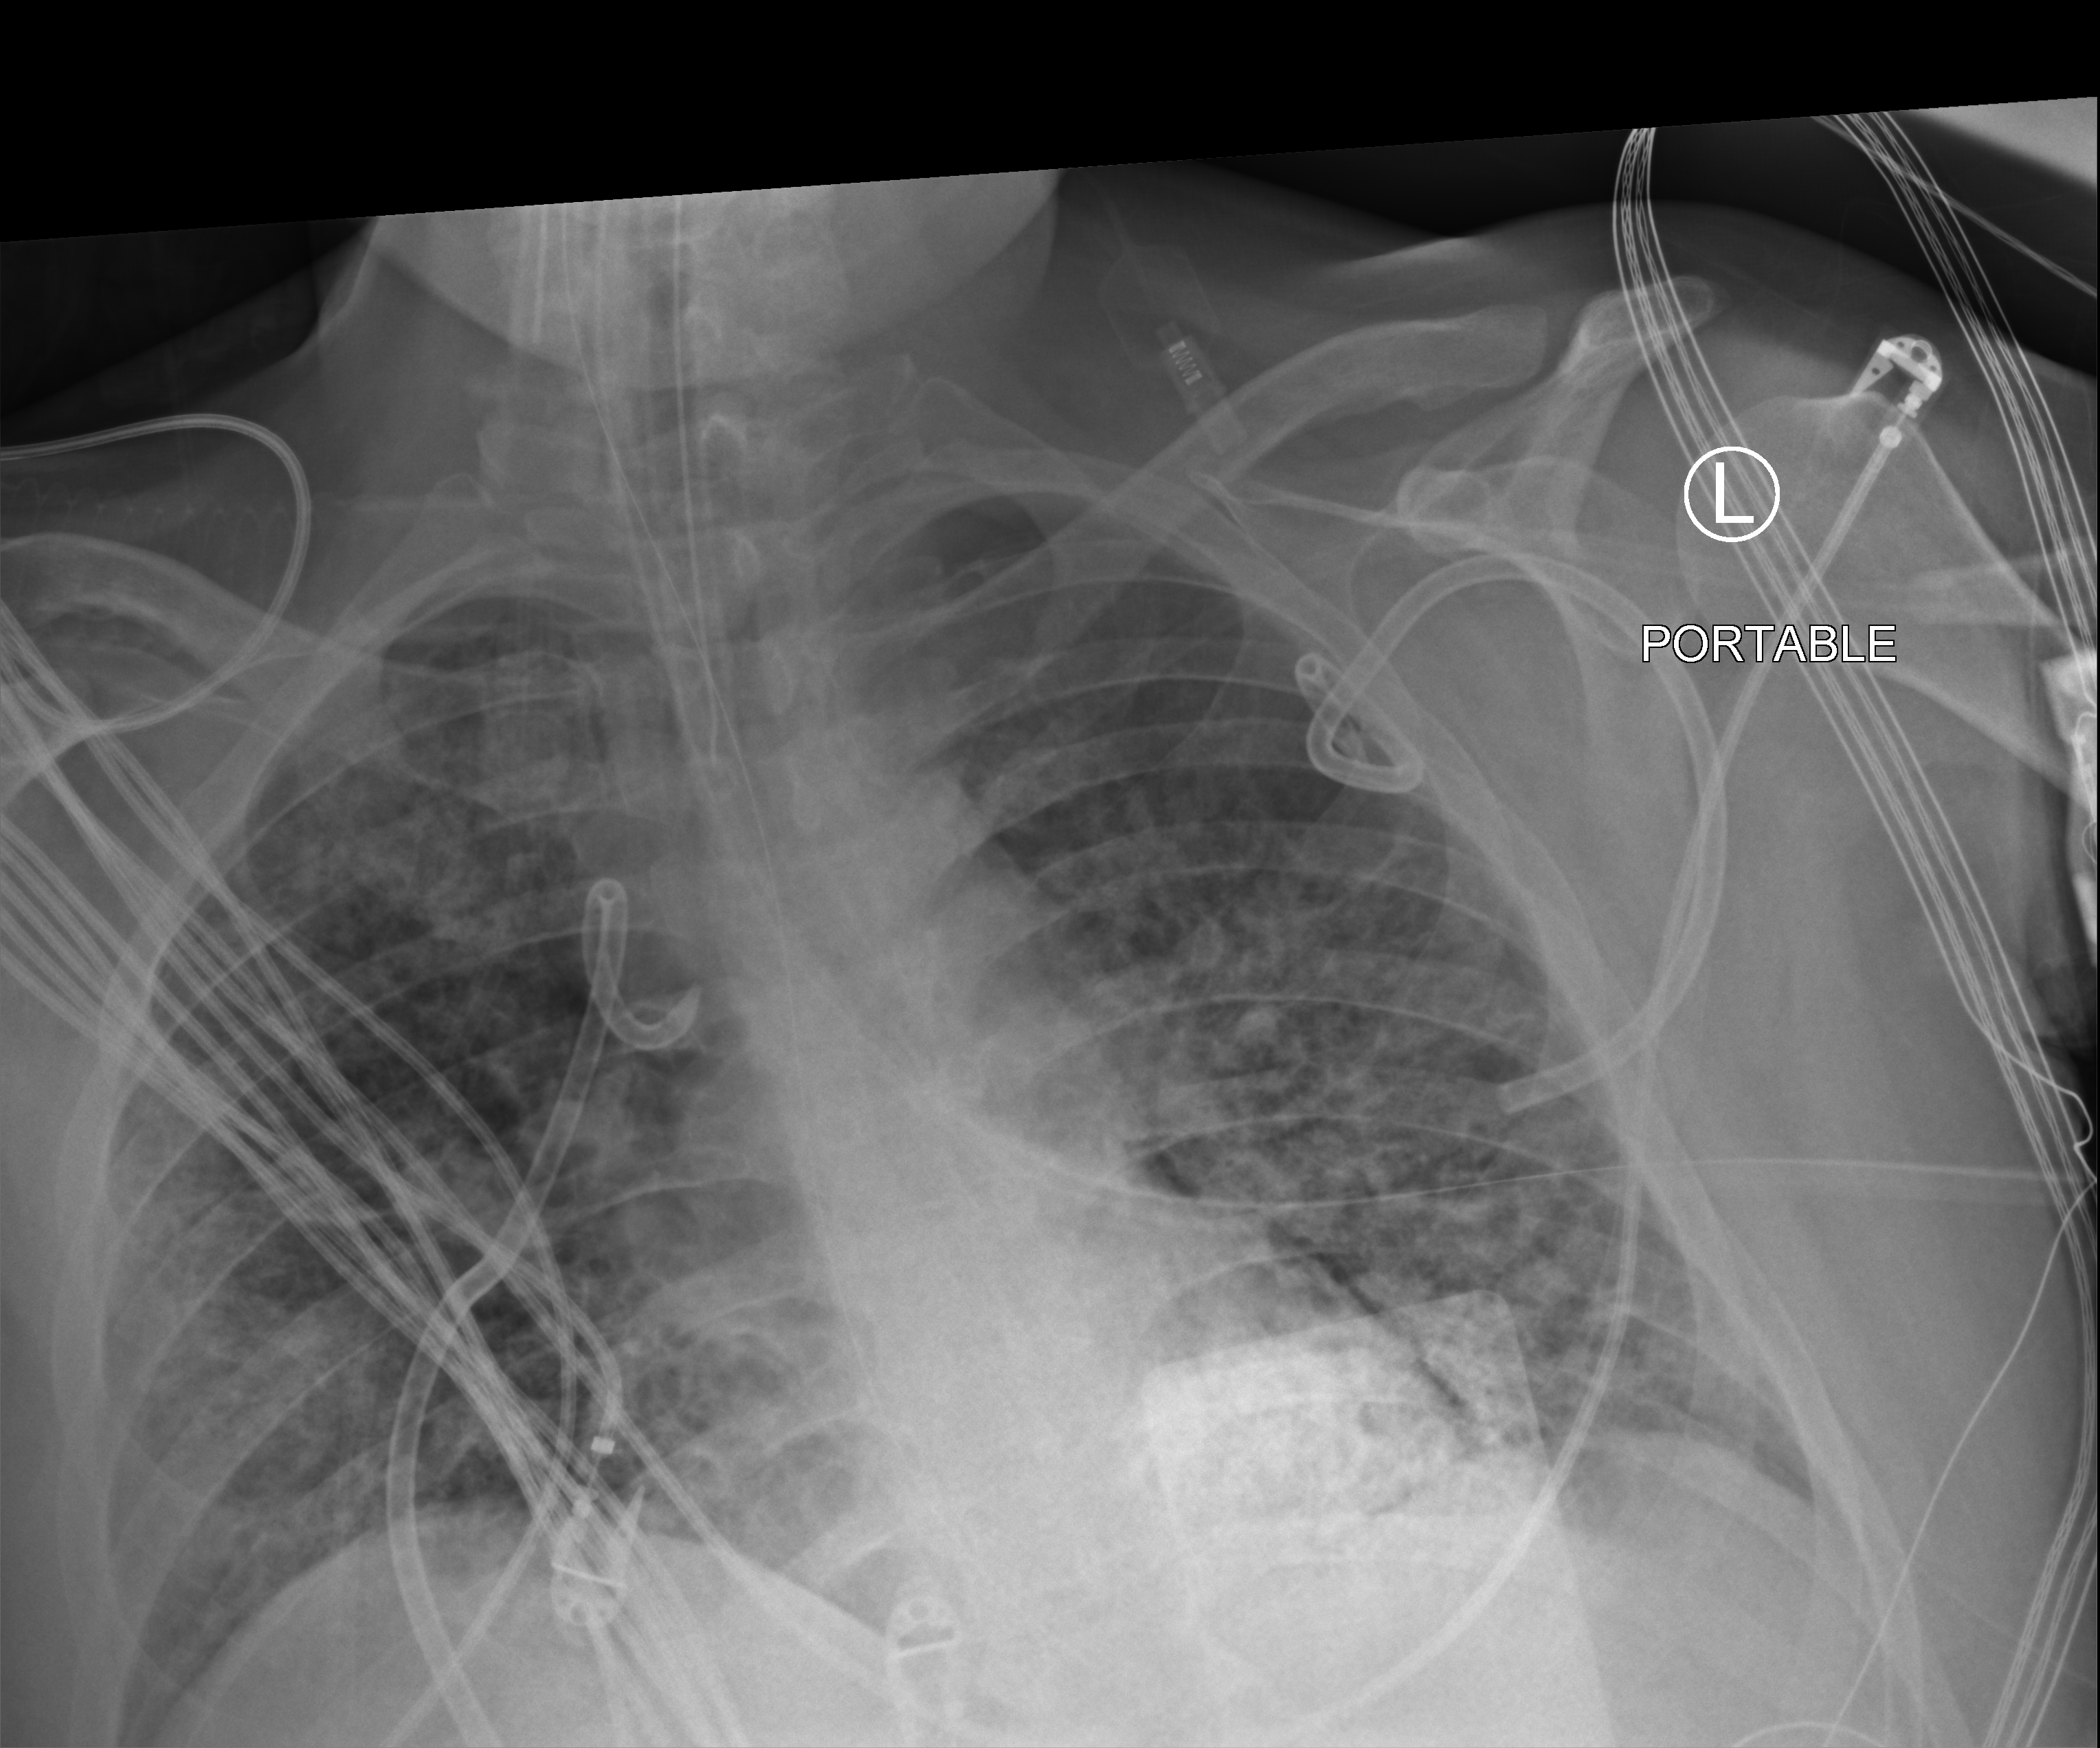
Bedside chest radiograph (computed radiography); anteroposterior (AP) projection. Patient hospitalised with COVID-19, aged 18–59 years.
Hospital-stay facts (about this admission, not read from this image; timing relative to this image not recorded): admitted to intensive care during this hospital stay: yes; length of hospital stay: 31 days; mechanically ventilated during this hospital stay: yes.